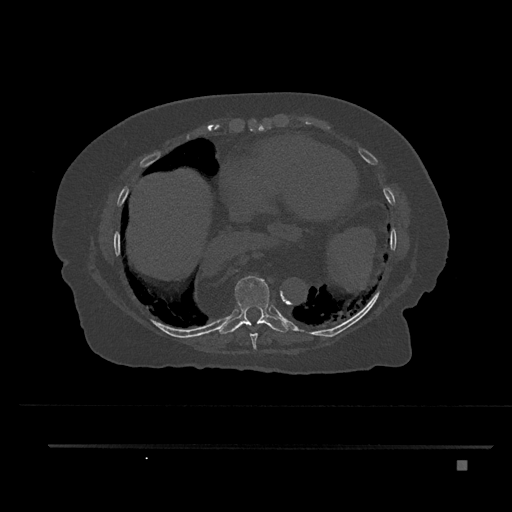
CT including the spine, one axial slice; position 412 of 797 along the scan axis; 120 kVp; bone window (W 1800 / L 400 HU); 0.5 mm slice thickness; 512 × 512 image matrix, field of view 437 × 437 mm. Patient: female, 76 years. Case-level facts recorded for this patient, not image findings: primary cancer: lung; vertebrae with lytic lesions (as recorded): T11, L3.
Annotated regions visible in this slice (semi-automatic segmentation, software-assisted and operator-edited):
- T8 vertebra: box from (x=250, y=333) to (x=258, y=350) px
- T9 vertebra: (x=218, y=276)–(x=289, y=335)